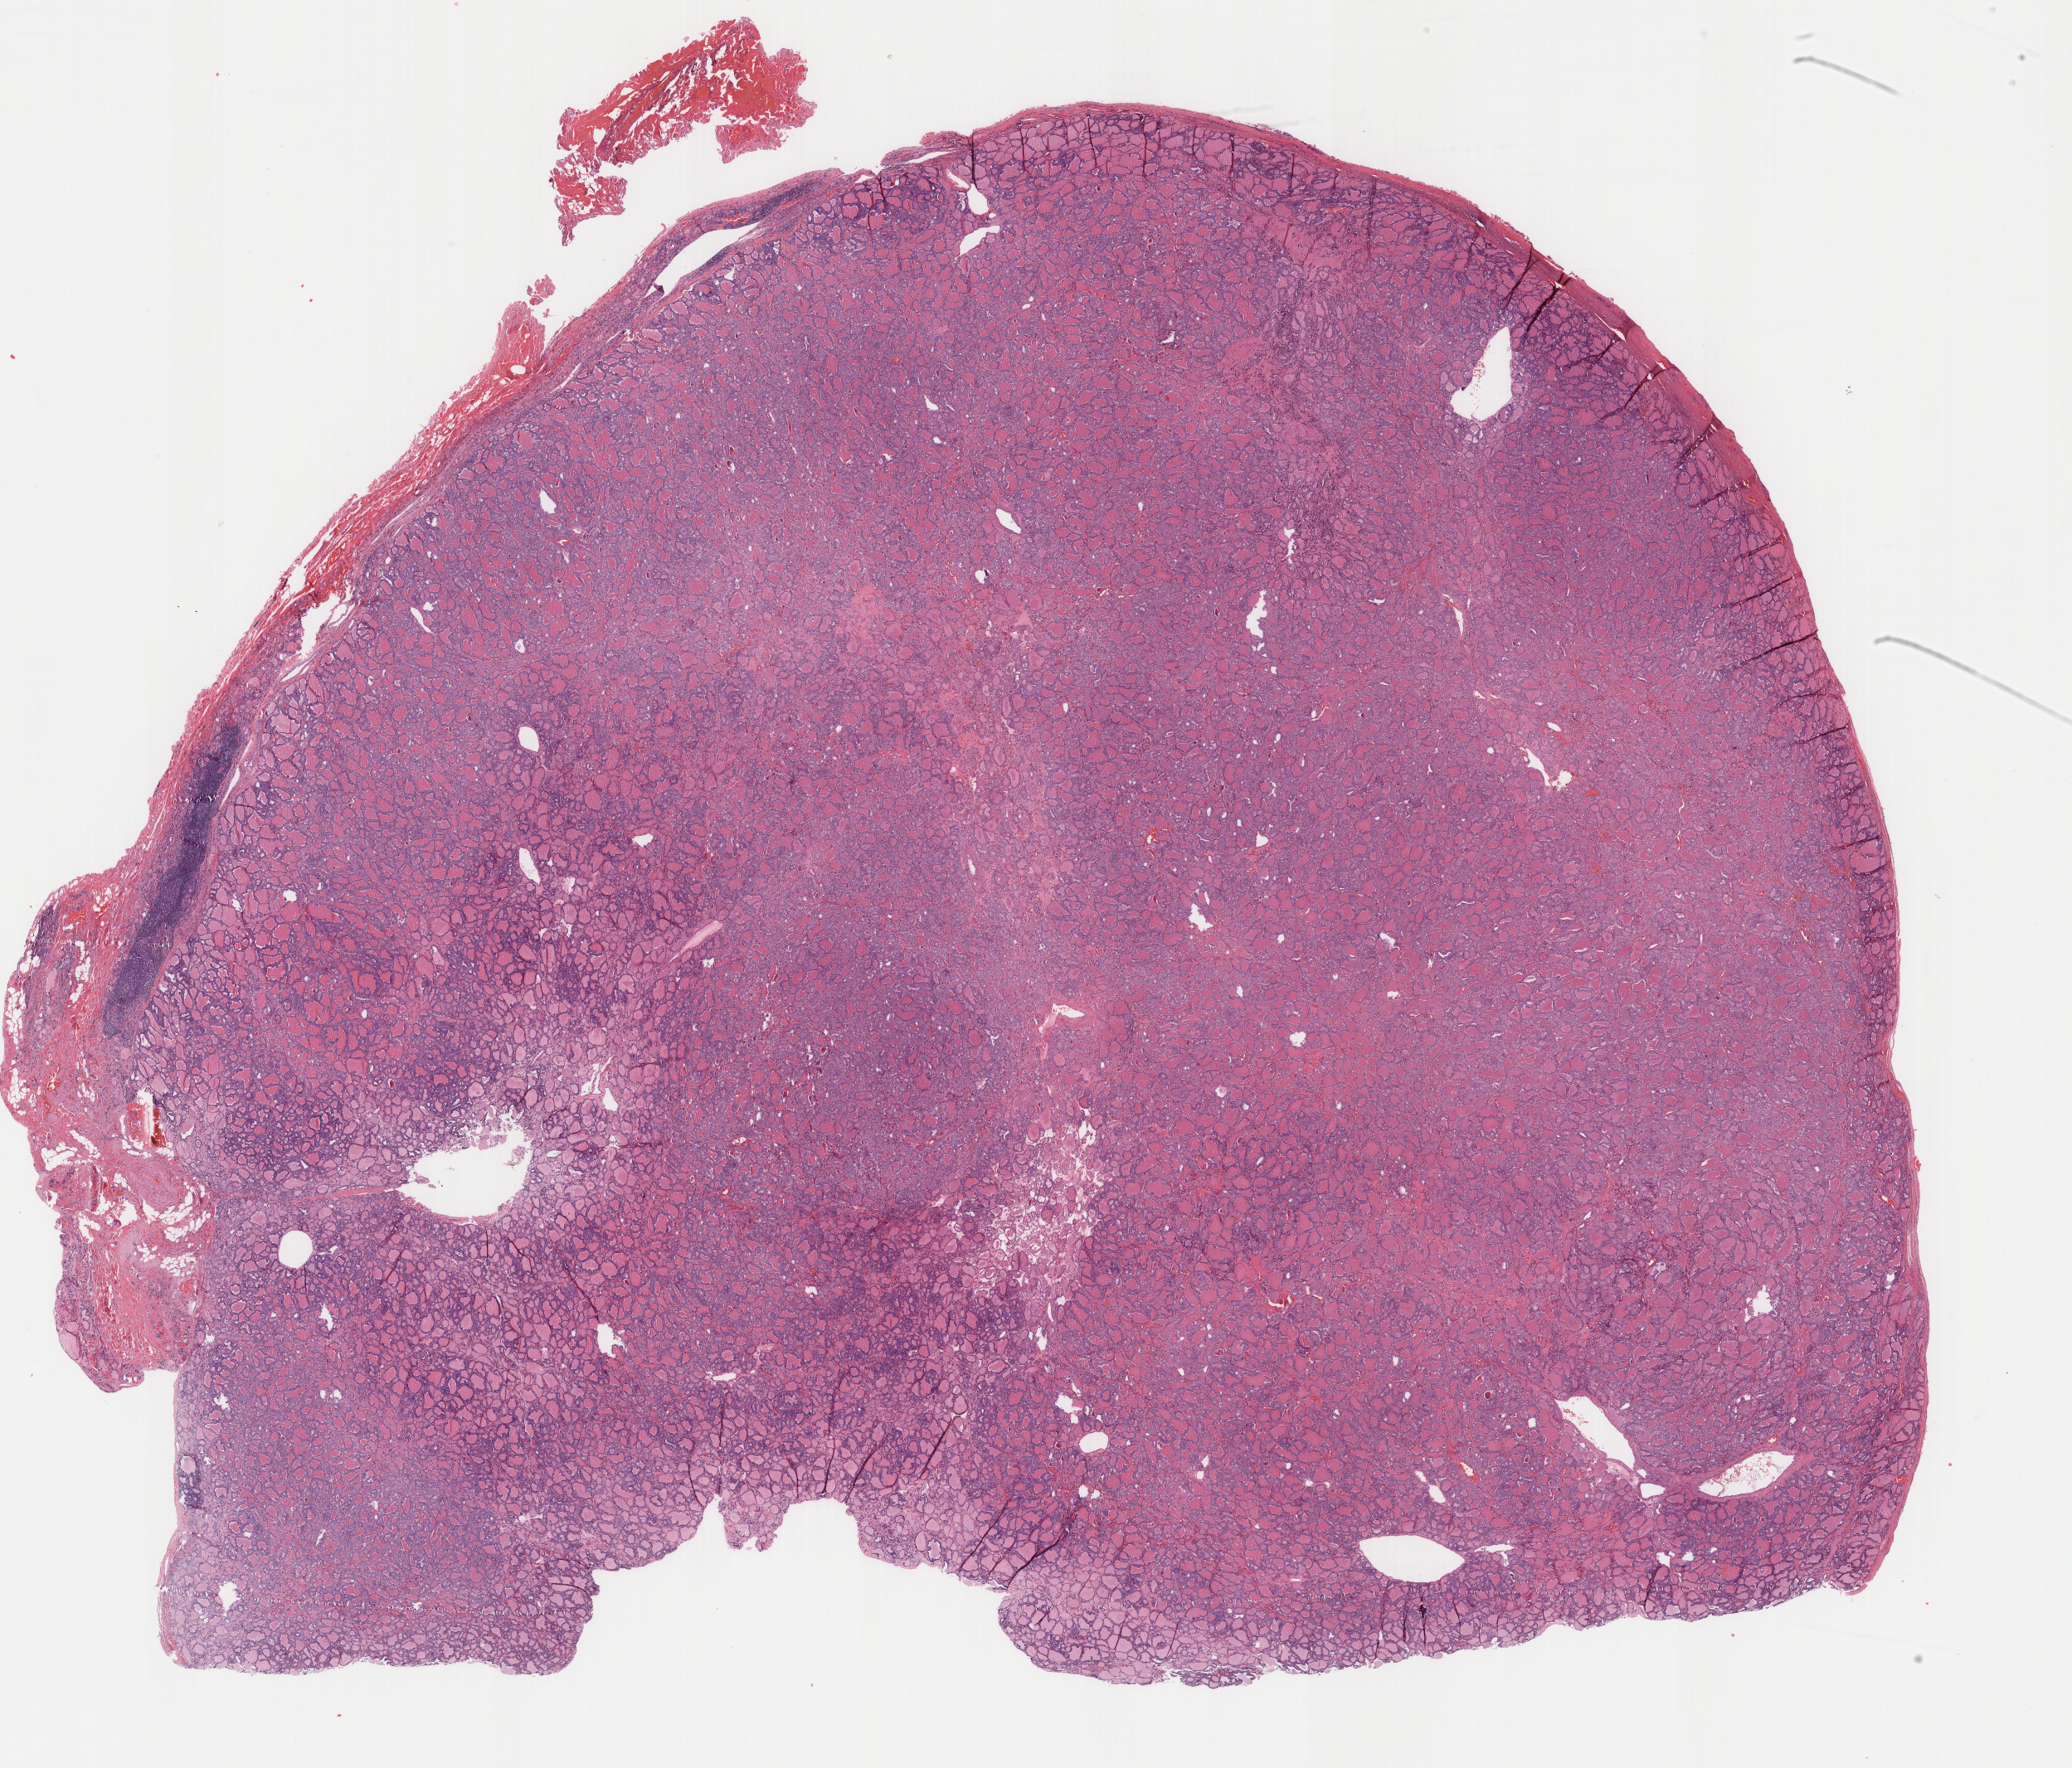
Hematoxylin and eosin (H&E) stained whole-slide image, whole scanned area (about 19.8 x 16.9 mm, from a 40x scan) shown as a low-resolution overview, FFPE section, sample: primary tumour, thyroid. Patient: female, age at initial diagnosis 31 years.
- diagnosis: Papillary adenocarcinoma, NOS (thyroid gland)
- AJCC pathologic stage: I (6th edition)
- lymph nodes positive (case pathology): 0 of 4 examined